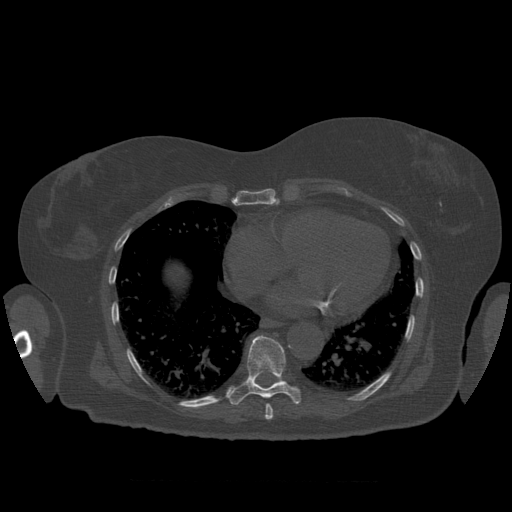
CT including the spine, one axial slice. Position 361 of 399 along the scan axis. Bone window (W 1800 / L 400 HU). 1.25 mm slice thickness. 512 × 512 image matrix, field of view 404 × 404 mm. Patient age 81 years. Case-level facts recorded for this patient, not image findings: primary cancer: renal.
Annotated regions visible in this slice (semi-automatic segmentation, software-assisted and operator-edited):
- T8 vertebra: bounding box [x1, y1, x2, y2] px = [265, 404, 274, 420]
- T9 vertebra: [226, 335, 301, 405]